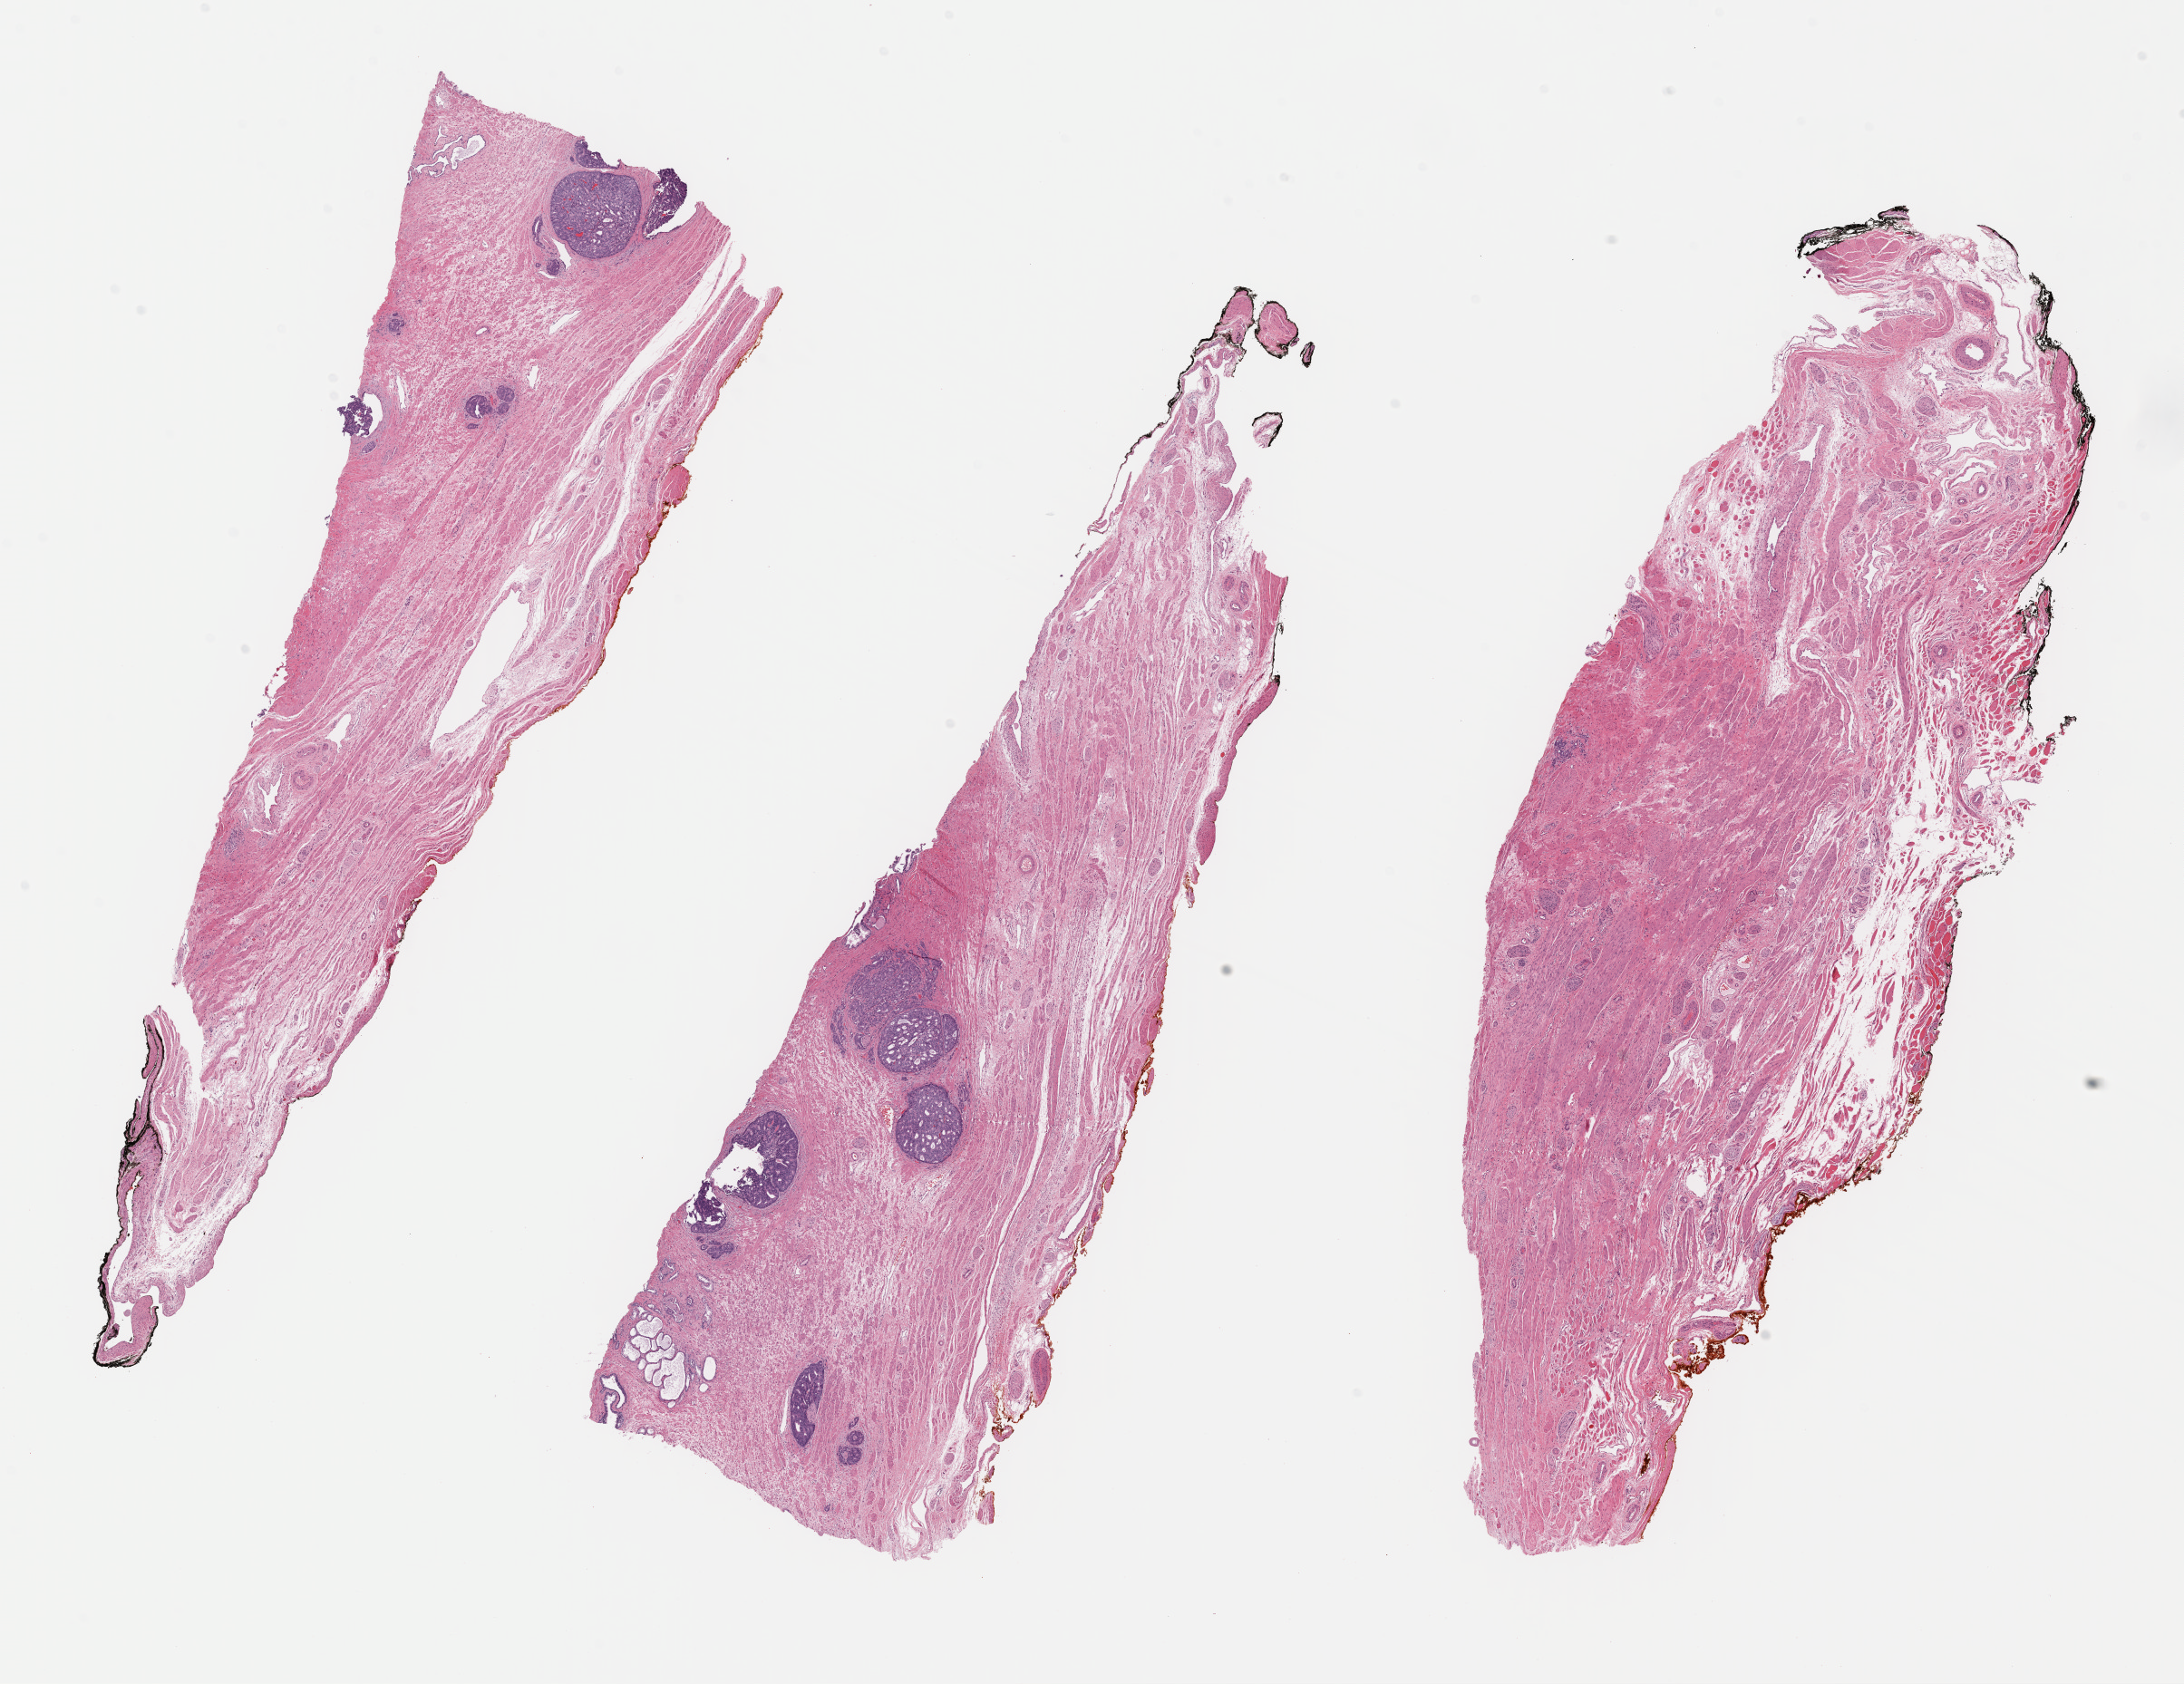
Whole-slide histology image, Hematoxylin and eosin (H&E) stained, low-resolution overview of the scanned area, about 18.9 x 14.6 mm (from a 40x scan), formalin-fixed paraffin-embedded (FFPE) diagnostic section, sample: primary tumour, prostate. Male patient; age at initial diagnosis 57 years. Gleason score: 8 (4+4).
* pathologic diagnosis: Adenocarcinoma, NOS (prostate gland)
* lymph nodes positive (case pathology): 1 of 23 examined